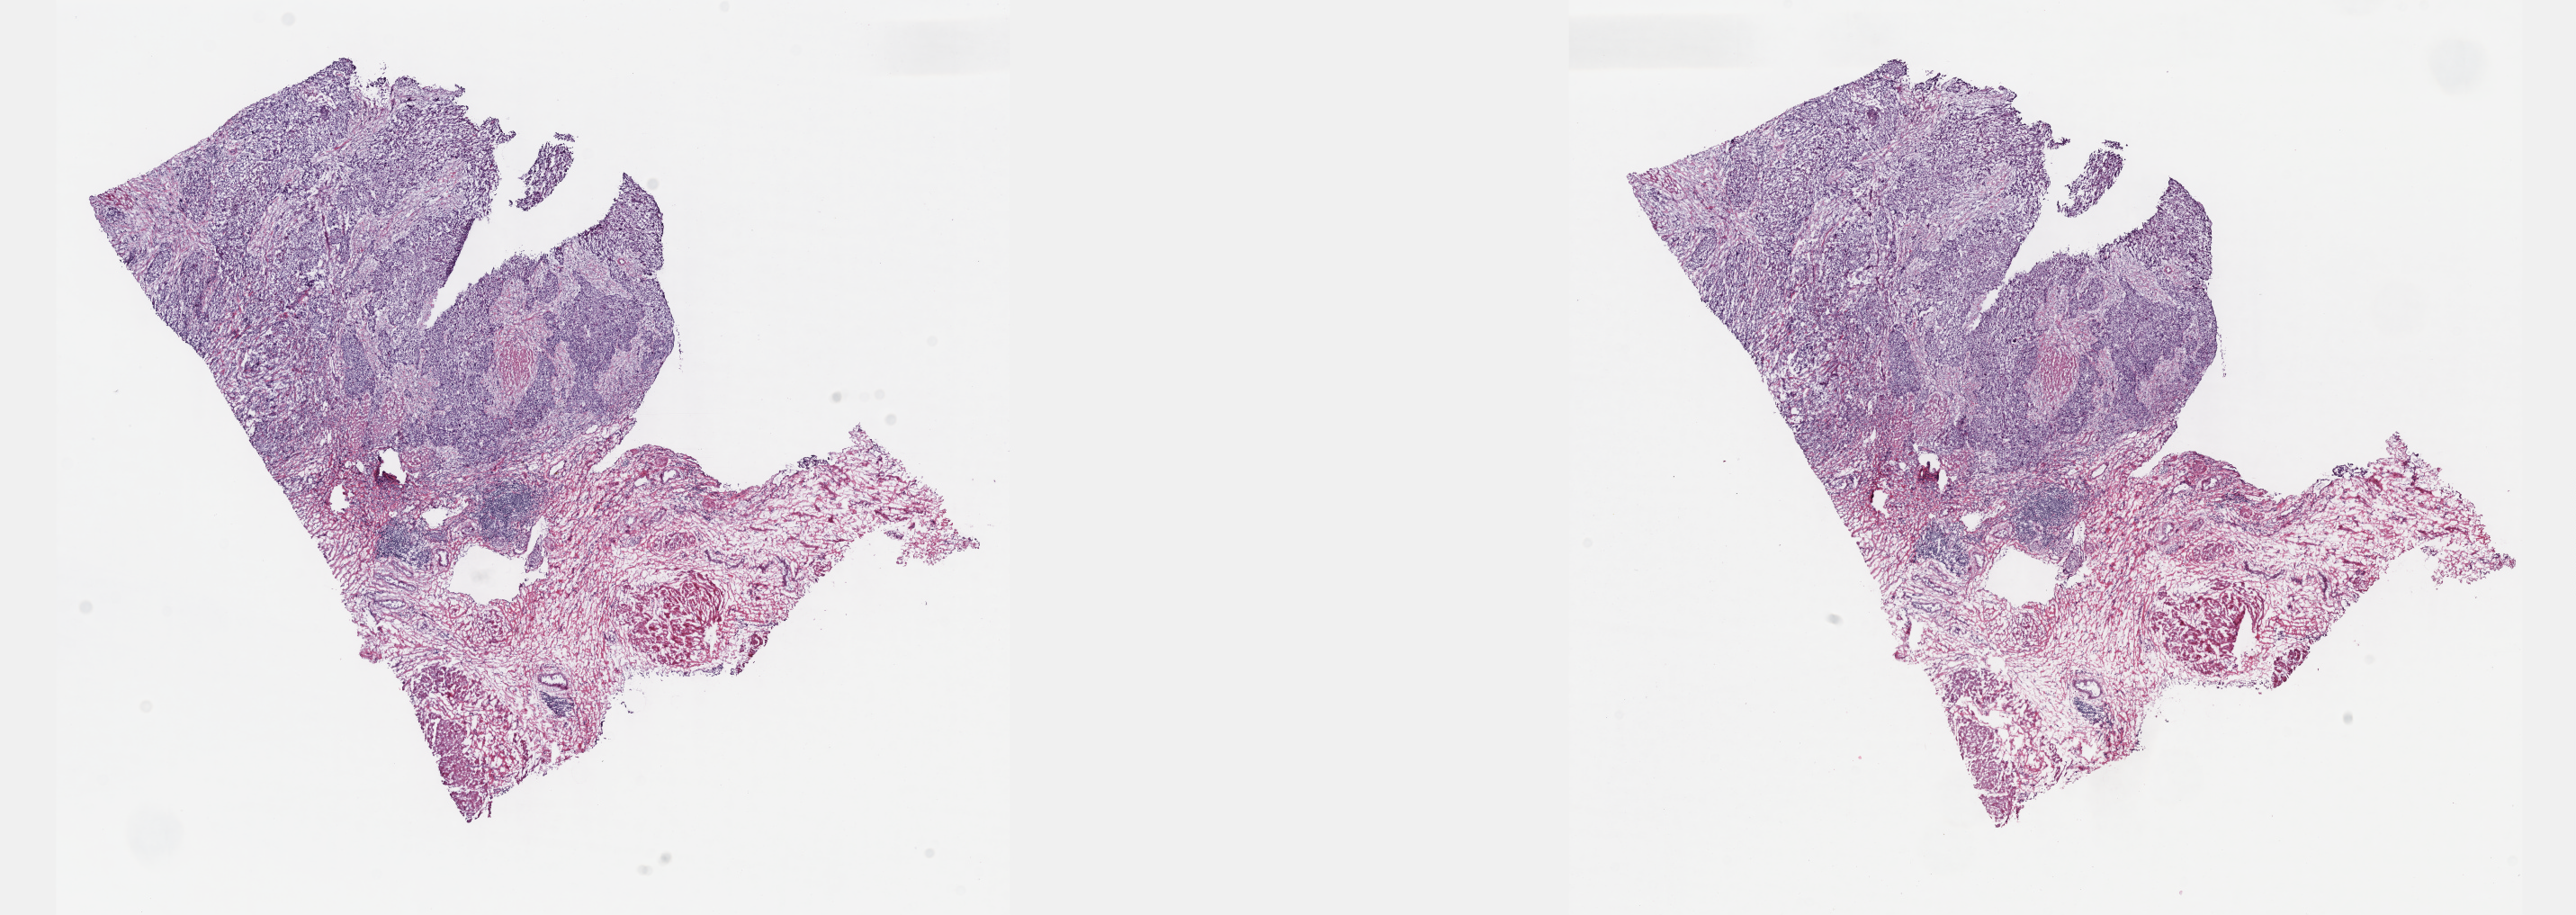
H&E whole-slide image — low-resolution overview of the scanned area, about 23.1 x 8.2 mm. Frozen section from the top of the tissue portion. Primary tumour sample from the bladder. Patient: female, age at initial diagnosis 64 years. Histologic grade: high grade. Pathologist review of this section (percent, as recorded): tumour cells 65%, tumour nuclei 65%, normal cells 0%, stromal cells 35%, necrosis 0%. Inflammatory infiltration, as recorded: lymphocyte infiltration 10%, monocyte infiltration 0%, neutrophil infiltration 0%.
• AJCC pathologic stage: II (6th edition)
• pathologic diagnosis: Transitional cell carcinoma
• lymph nodes positive (case pathology): 0 of 76 examined